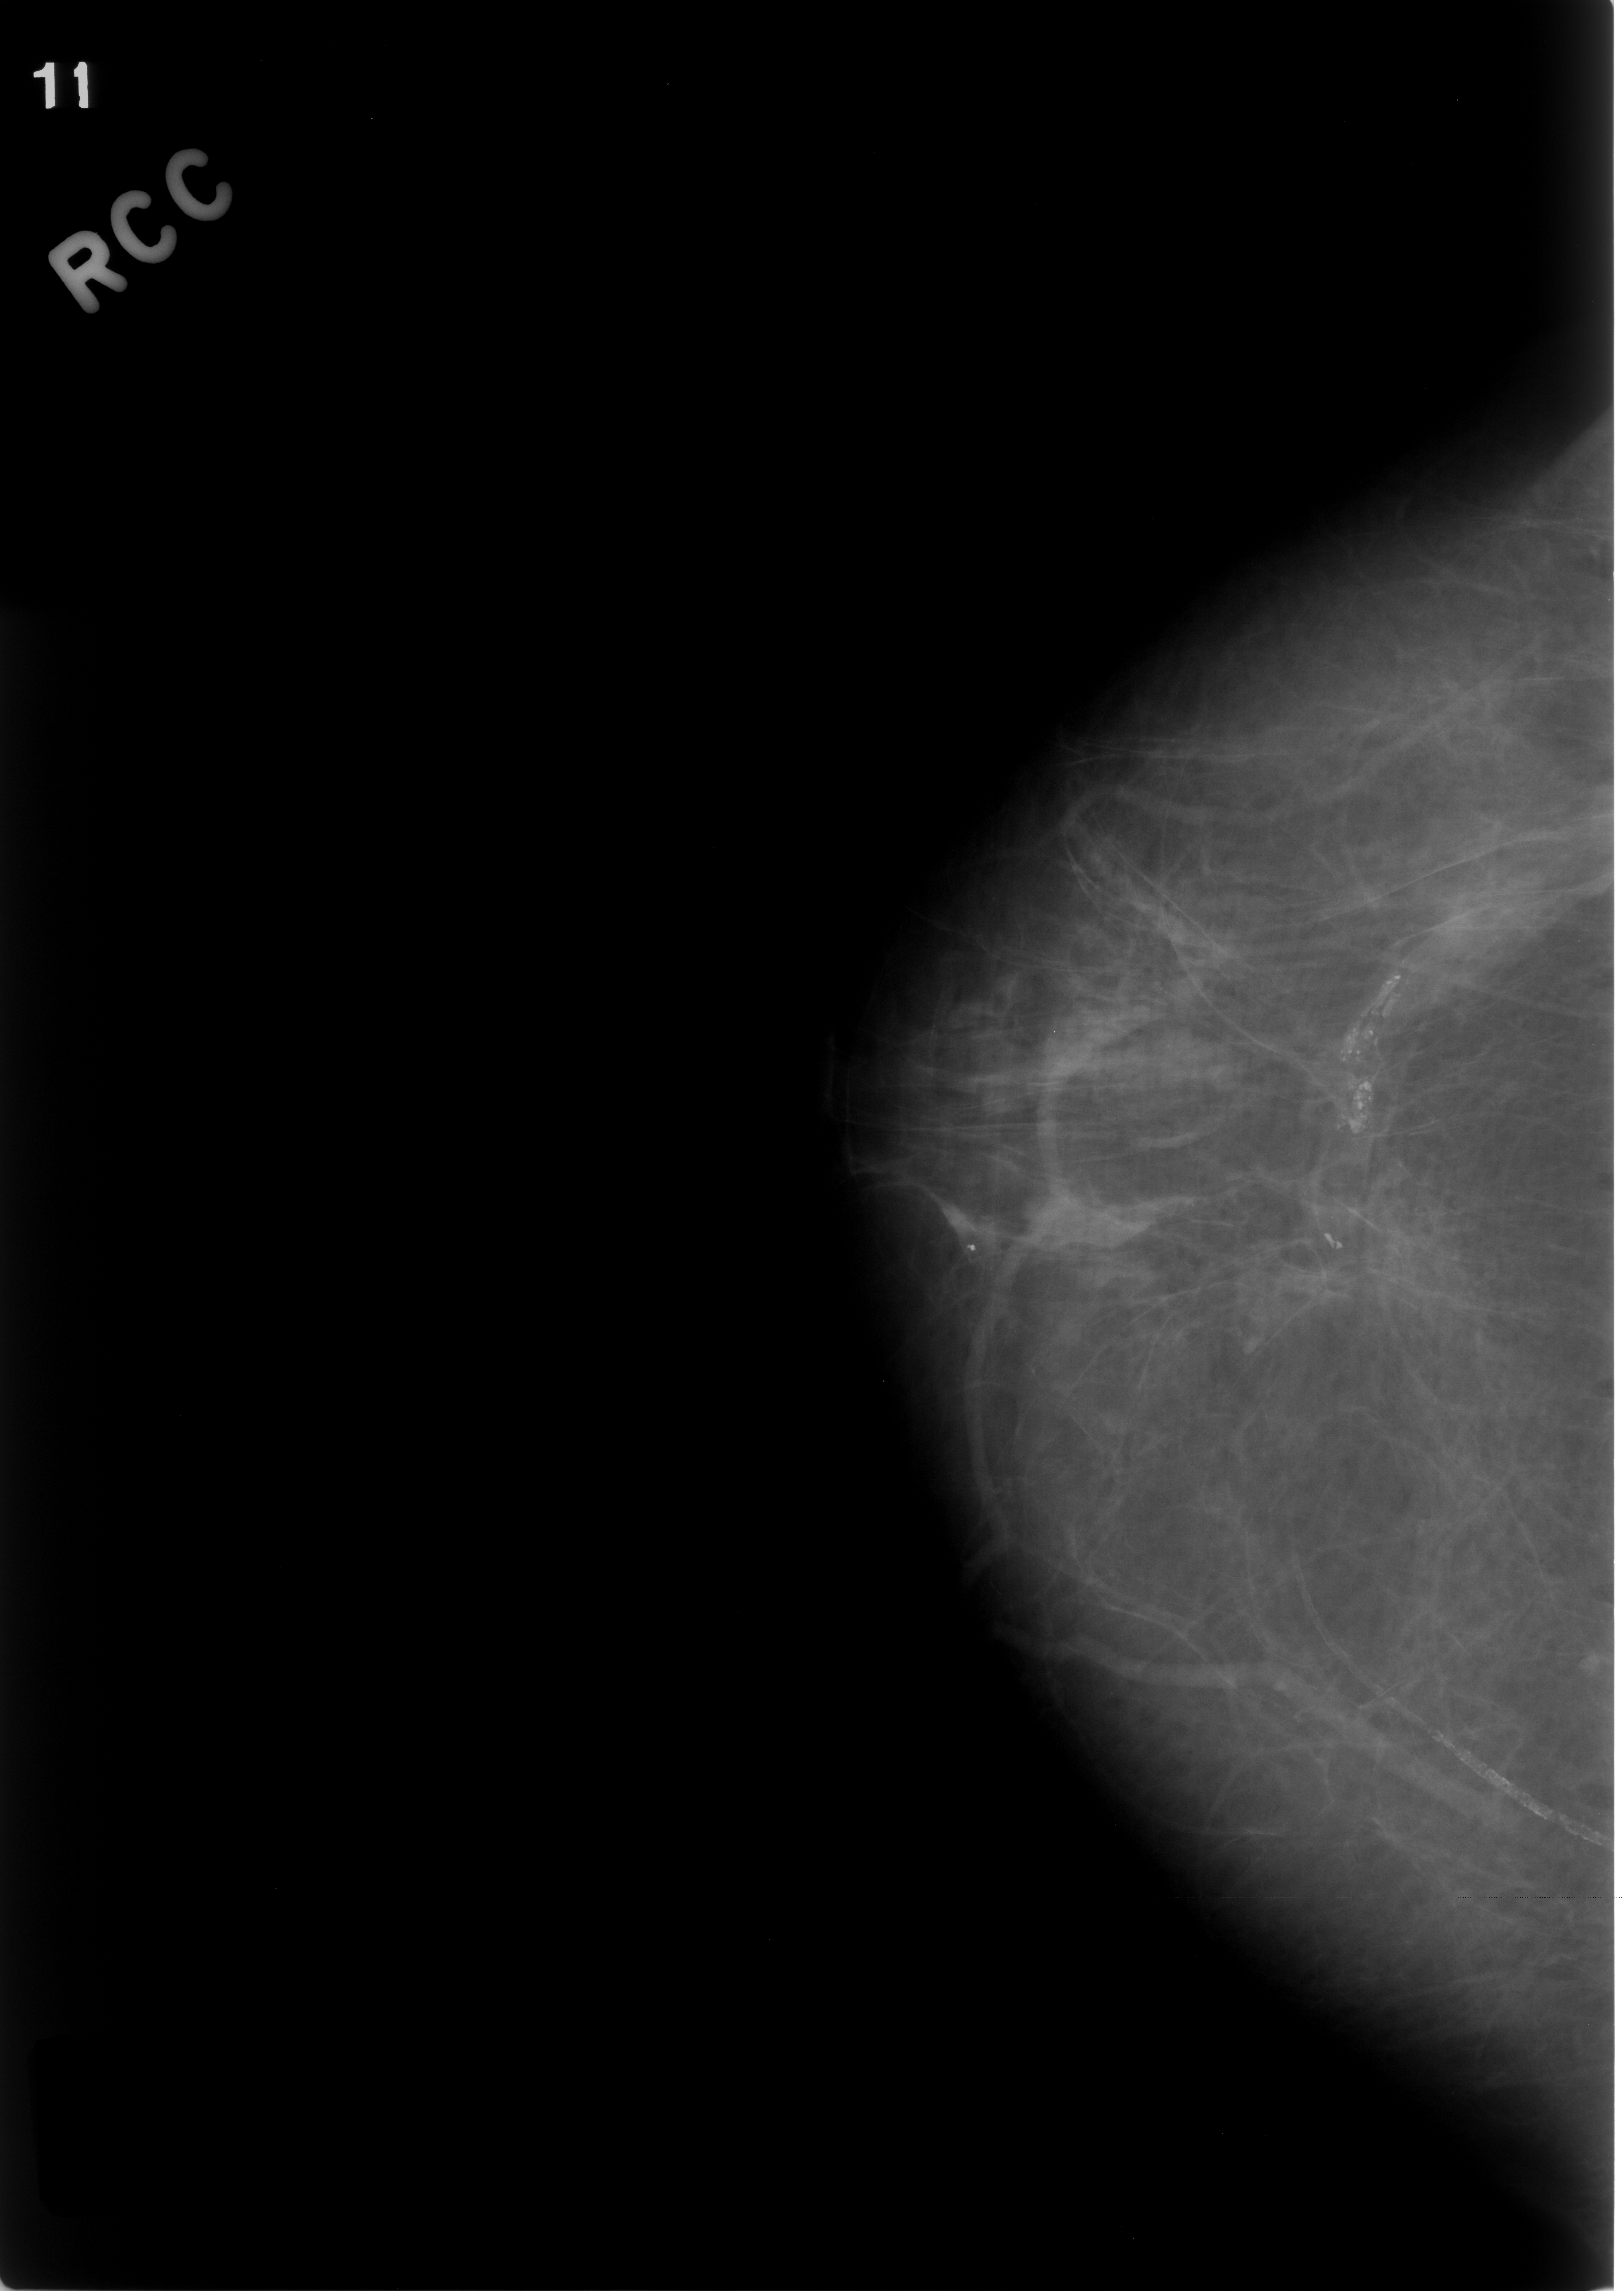
Mammogram (digitized film); right breast; craniocaudal (CC) view; breast composition: almost entirely fatty (BI-RADS density category 1 of 4); 1624 × 2291 image matrix.
Expert-marked regions of interest on this image (one box per marked abnormality):
- calcifications, morphology pleomorphic, distribution segmental; BI-RADS assessment category 4; subtlety rating 5 on a 1 (subtle) to 5 (obvious) scale; pathology (as recorded): benign: bounding box (x1, y1, x2, y2) in pixels: (1228, 899, 1494, 1331)